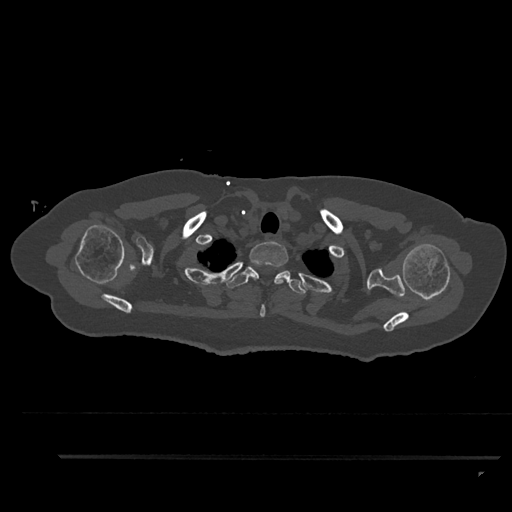
CT including the spine, one axial slice; position 741 of 797 along the scan axis; 120 kVp; bone window (W 1800 / L 400 HU); 512 × 512 image matrix. Patient: female, 44 years. From the clinical record (not read from this slice): primary cancer: renal; vertebrae with lytic lesions (as recorded): L1.
Structures marked on this image (semi-automatic segmentation, software-assisted and operator-edited):
- T1 vertebra: bounding box [x1, y1, x2, y2] px = [248, 241, 289, 317]
- T2 vertebra: [226, 265, 306, 295]